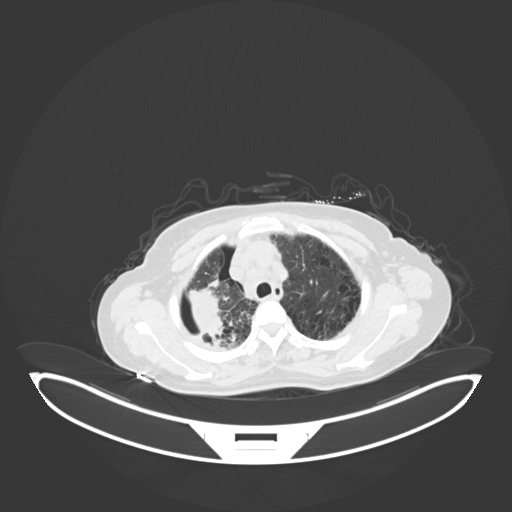
Chest CT, one axial slice. Position 50 of 69 along the scan axis. Reconstruction kernel B30f. 120 kVp. Lung window (W 1500 / L -600 HU). 3 mm slice thickness. 512 × 512 image matrix. Female patient, age 64 years. From the clinical record (not read from this slice): clinical TNM (as recorded): T3 N3 M0.
Structures marked on this image (rectangle marked by the reading radiologist):
- lung tumour (recorded histology: squamous cell carcinoma): bounding box <180,282,226,344> (left, top, right, bottom; pixels)